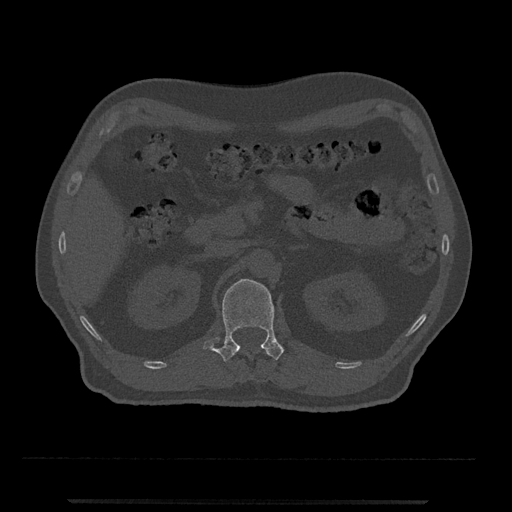
CT including the spine, one axial slice. Position 349 of 797 along the scan axis. 120 kVp. Bone window (W 1800 / L 400 HU). 0.5 mm slice thickness. 512 × 512 image matrix. Male patient, age 63 years. From the clinical record (not read from this slice): primary cancer: prostate.
Outlined on this slice (semi-automatic segmentation, software-assisted and operator-edited):
- L1 vertebra: box from (x=203, y=279) to (x=284, y=362) px
- T12 vertebra: (x=265, y=351)–(x=268, y=355)